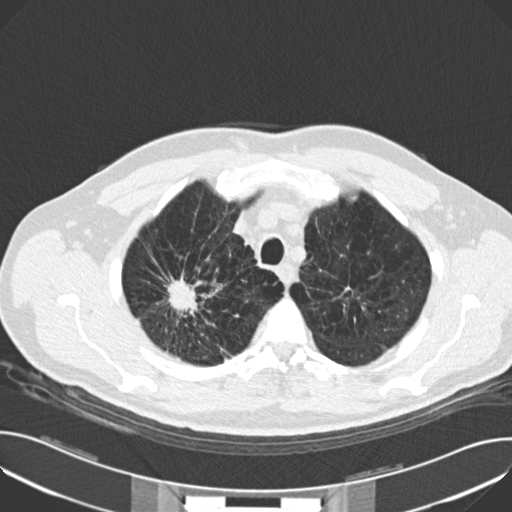
Low-dose screening chest CT, one axial slice. Slice 134 of 159 in the series (ordered by position). Reconstruction kernel B30f. 120 kVp. Lung window (W 1500 / L -600 HU). 2 mm slice thickness. 512 × 512 image matrix, field of view 380 × 380 mm.
Annotated regions visible in this slice (expert manual segmentation):
- lesion 1 (tumor, upper lobe of right lung): box from (x=166, y=276) to (x=197, y=316) px